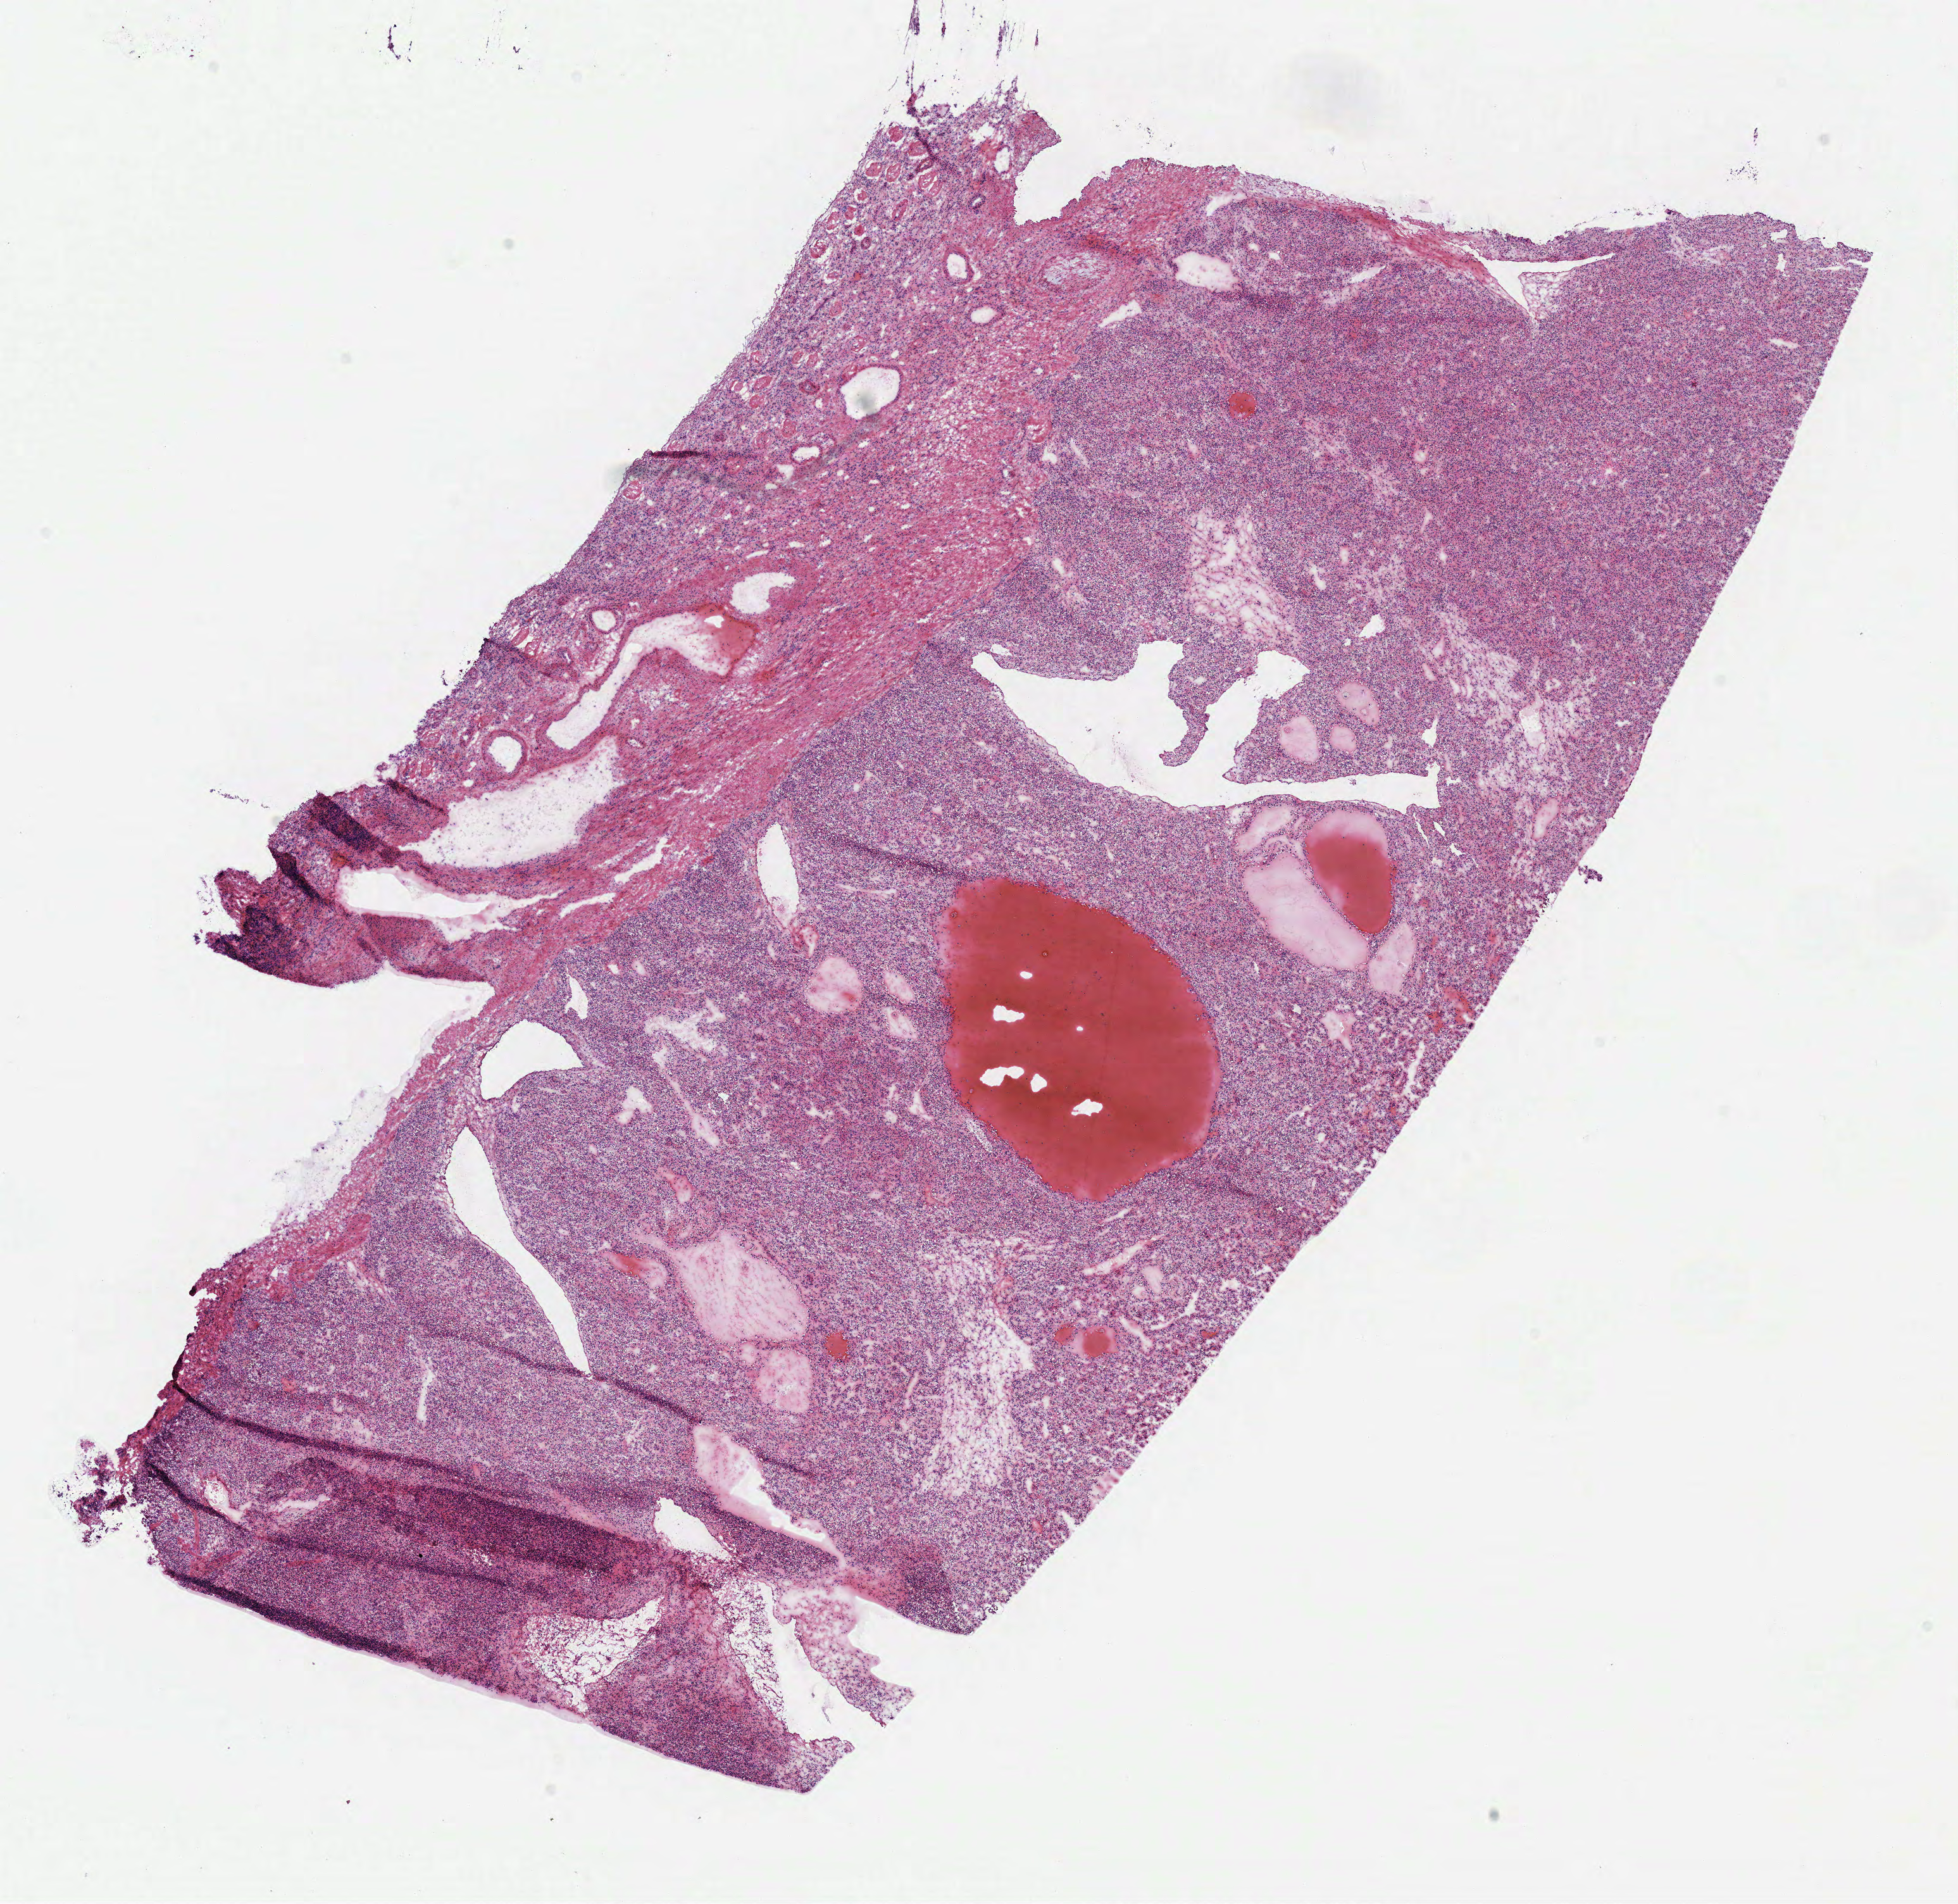
Whole-slide histology image, Hematoxylin and eosin (H&E) stained — low-resolution overview of the scanned area, about 12.2 x 11.8 mm, frozen section, sample: primary tumour, kidney. Patient: male, age at initial diagnosis 60 years. Histologic grade: G2 (moderately differentiated). Composition of this section per pathologist review: tumour cells 82%, tumour nuclei 80%, normal cells 18%, stromal cells 10%, necrosis 0%.
Diagnosis: Clear cell adenocarcinoma, NOS. TNM: T1b N0 M0. AJCC pathologic stage: I. Lymph nodes positive (case pathology): 0 of 10 examined.